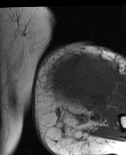
MRI of an extremity soft-tissue mass, one axial slice. Position 22 of 86 along the scan axis. MR volume resampled by the dataset authors to the PET/CT grid (not the native acquisition matrix). 3.27 mm slice thickness. 126 × 155 image matrix, field of view 123 × 151 mm. Female patient. Case-level facts recorded for this patient, not image findings: histological type: pleiomorphic leiomyosarcoma; grade: high; site of the primary tumour: left biceps.
Annotated regions visible in this slice (expert contour drawn on MRI and transferred to this co-registered scan by the dataset authors):
- gross tumour volume including surrounding oedema: bounding box <47,54,117,112> (left, top, right, bottom; pixels)
- gross tumour volume (mass): <47,54,115,105>